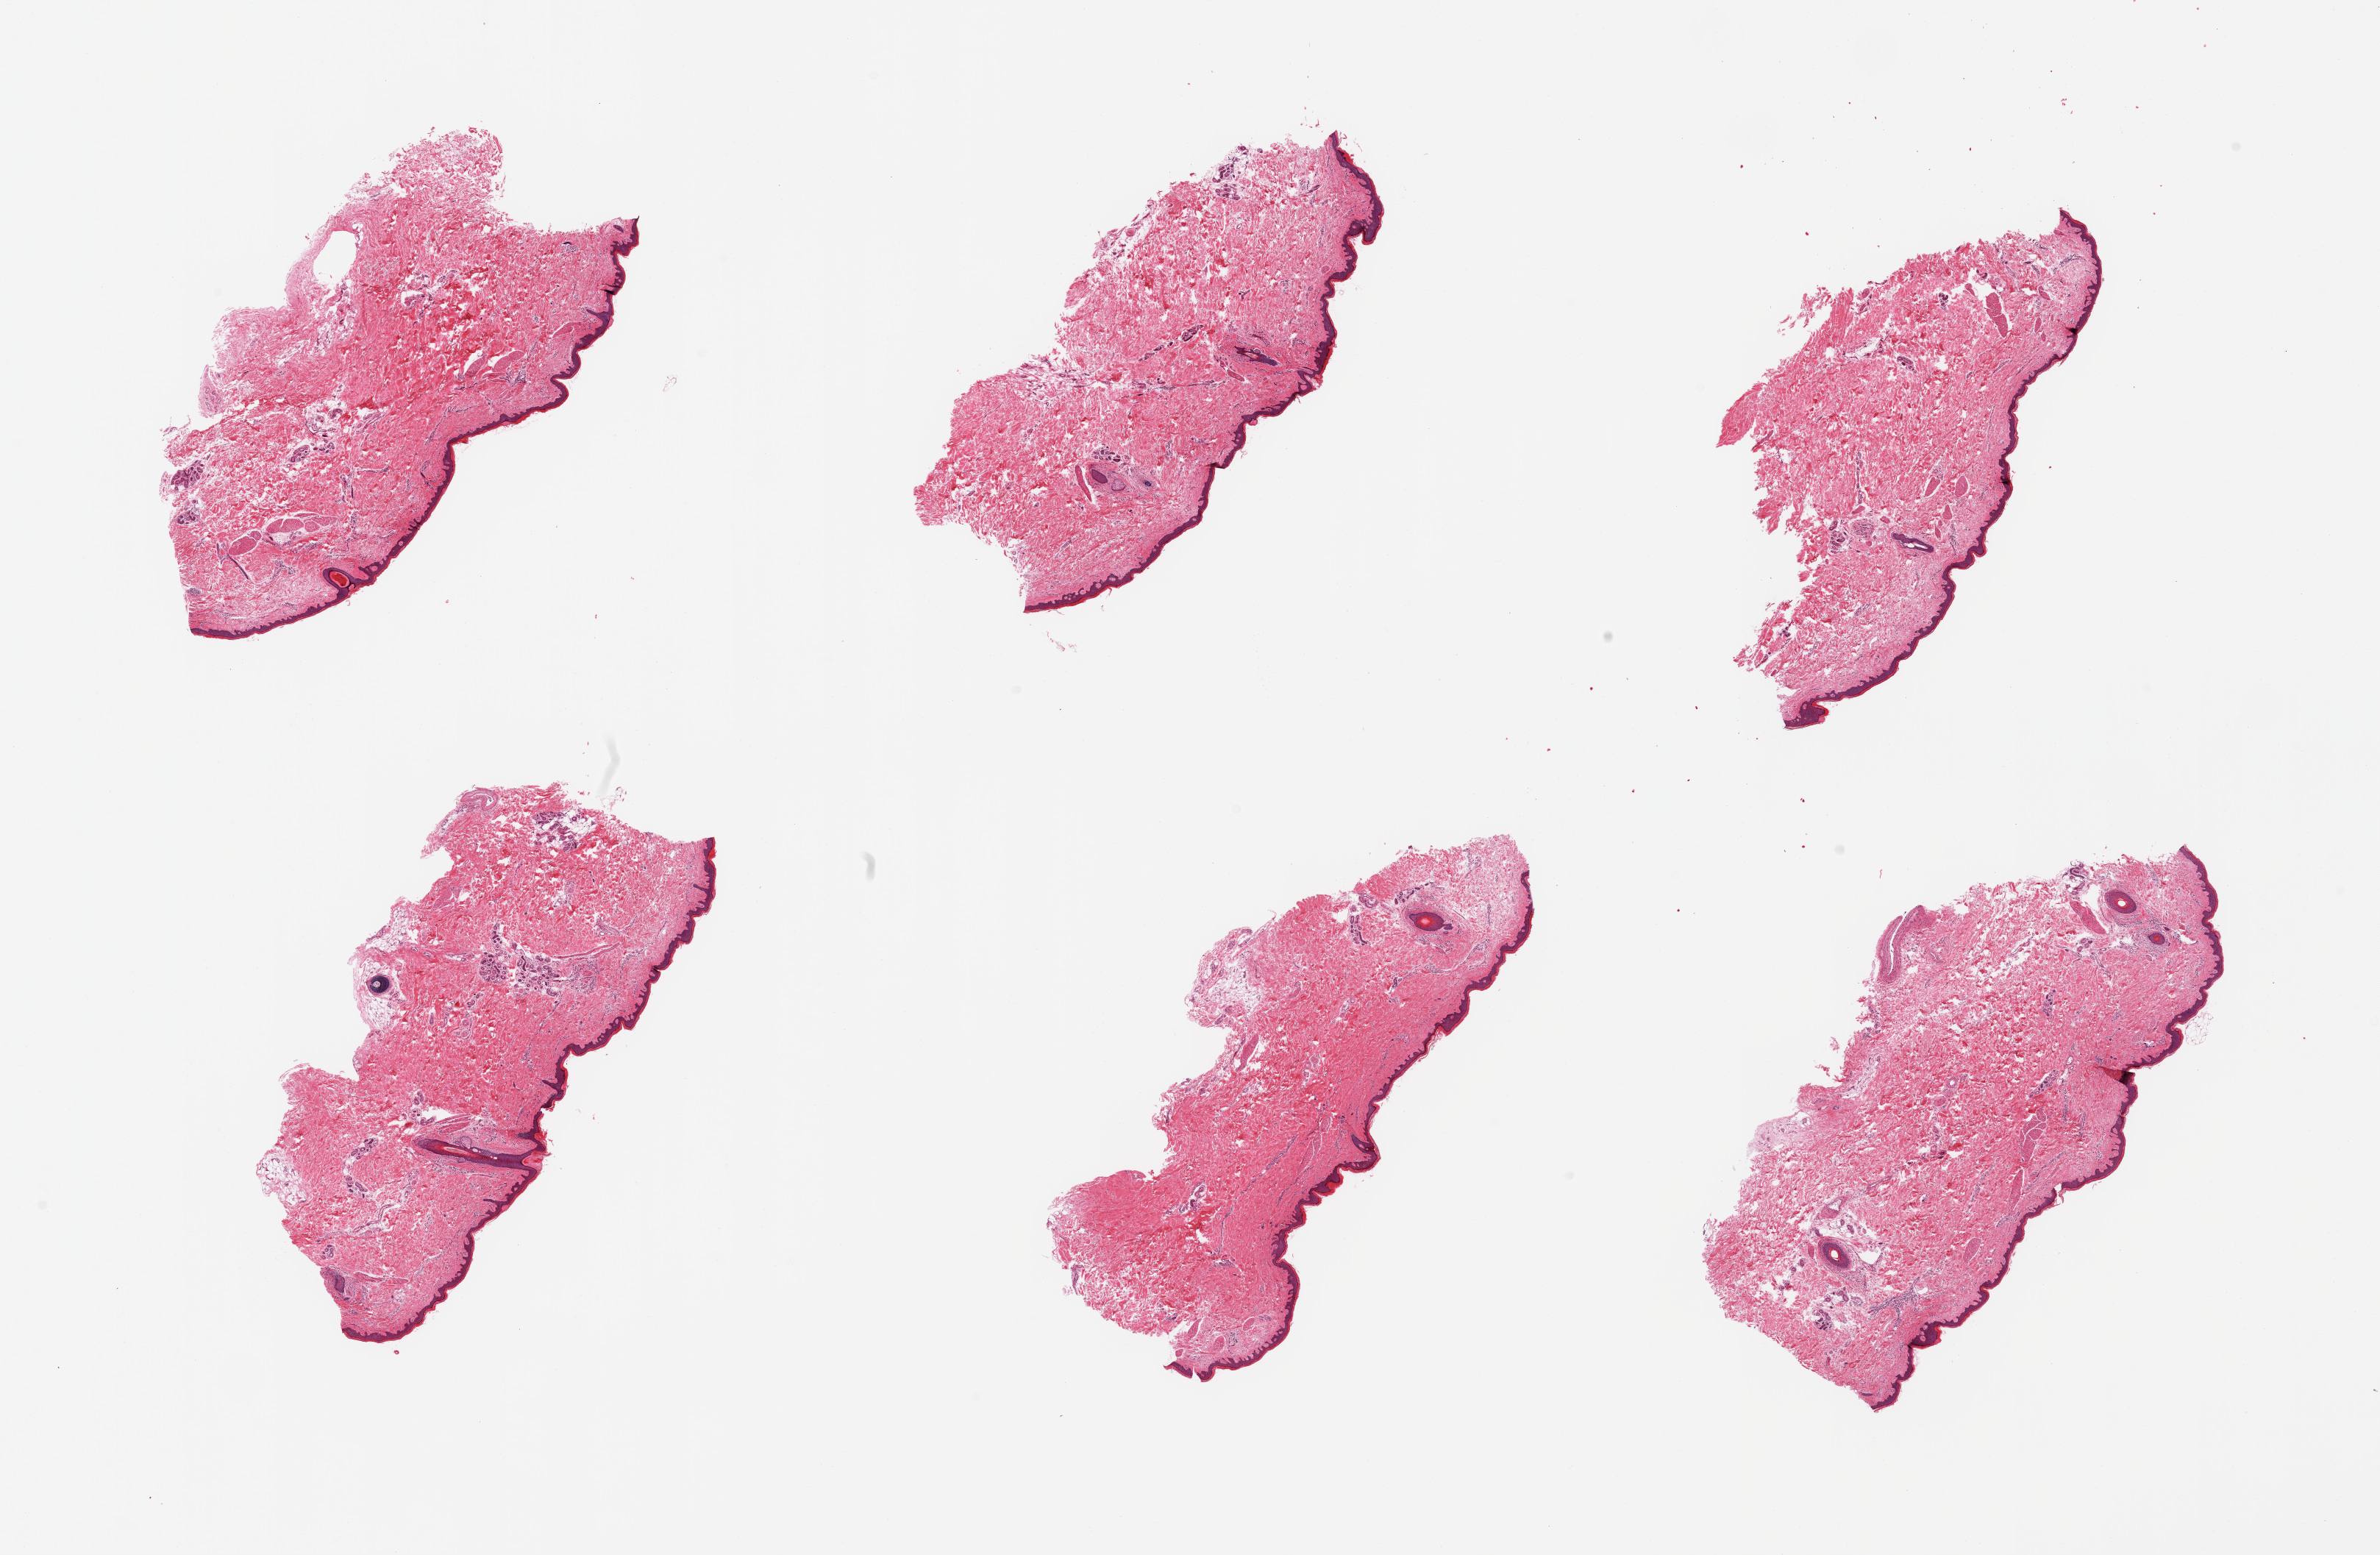
Digitized haematoxylin and eosin-stained section, brightfield, low-resolution overview of the scanned area, about 25.6 x 16.7 mm (acquisition: 20x scan), PAXgene-fixed, paraffin-embedded tissue, sampled site (target tissue): skin of lower leg, donor tissue sample. Donor: male.
Pathologist's review note for this sample: 6 pieces; well trimmed;dermal fat <5%.